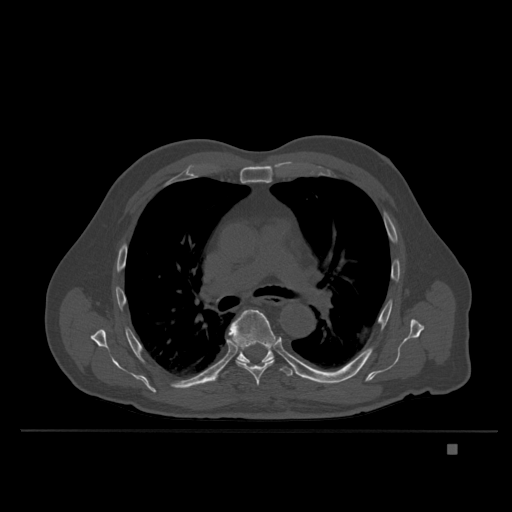
CT including the spine, one axial slice. Bone window (W 1800 / L 400 HU). 512 × 512 image matrix, field of view 434 × 434 mm. Male patient, age 73 years. Case-level facts recorded for this patient, not image findings: primary cancer: skin.
Structures marked on this image (semi-automatically segmented with operator editing):
- T6 vertebra: bounding box (x1, y1, x2, y2) in pixels: (228, 309, 275, 386)
- T7 vertebra: (214, 343, 299, 381)